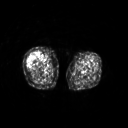
FDG PET of an extremity soft-tissue mass (from a PET/CT study), one axial slice. Slice 214 of 311 in the series (ordered by position). 128 × 128 image matrix. Female patient, age 57 years. From the clinical record (not read from this slice): histological type: pleiomorphic undifferentiated sarcoma; grade: high; site of the primary tumour: right quadricep.
Annotated regions visible in this slice (expert contour drawn on MRI and transferred to this co-registered scan by the dataset authors):
- tumour plus oedema (research contour): bounding box [x1, y1, x2, y2] px = [27, 52, 41, 66]